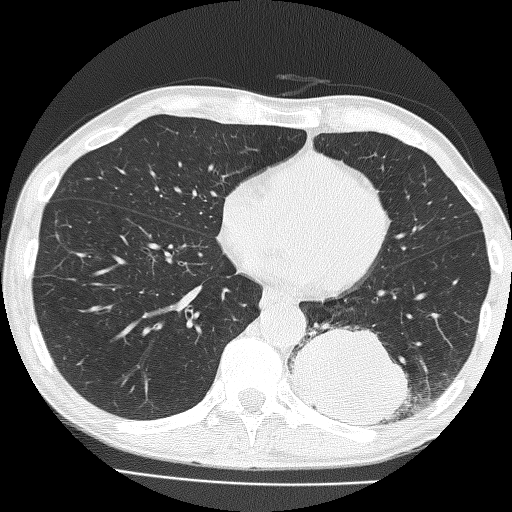
Chest CT (low-dose screening protocol), one axial image. Baseline screening round. Lung window (W 1500 / L -600 HU). 2 mm slice thickness. Lung (sharp) reconstruction kernel (FC51). Slice 98 of 160 in the series. Male participant, aged 58 years at enrolment. Current smoker at enrolment.
Expert-annotated lung lesion, bounding box (x1, y1, x2, y2) in pixels: (296, 303, 425, 434). The screening reader recorded 2 non-calcified nodules or masses ≥4 mm on this exam (left lower lobe, left upper lobe); which of them this box marks is not recorded. Lung cancer was diagnosed 39 days after this screen: non-small cell carcinoma, left lower lobe, poorly differentiated (G3), stage IV (AJCC 6th edition), 74 mm at pathology.